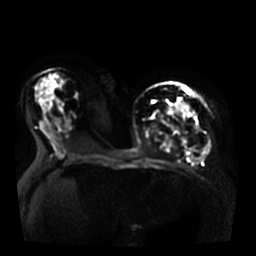
Breast MRI, one axial slice. Slice 19 of 36 in the series (ordered by position). Diffusion-weighted series; image 2 of 4 stored at this slice position (different b-values; order by instance number). 3 T. 5 mm slice thickness. 256 × 256 image matrix, field of view 350 × 350 mm. Female patient.
Structures marked on this image (outlined manually by an expert reader):
- tumour on diffusion-weighted imaging: bounding box [x1, y1, x2, y2] px = [180, 102, 189, 112]